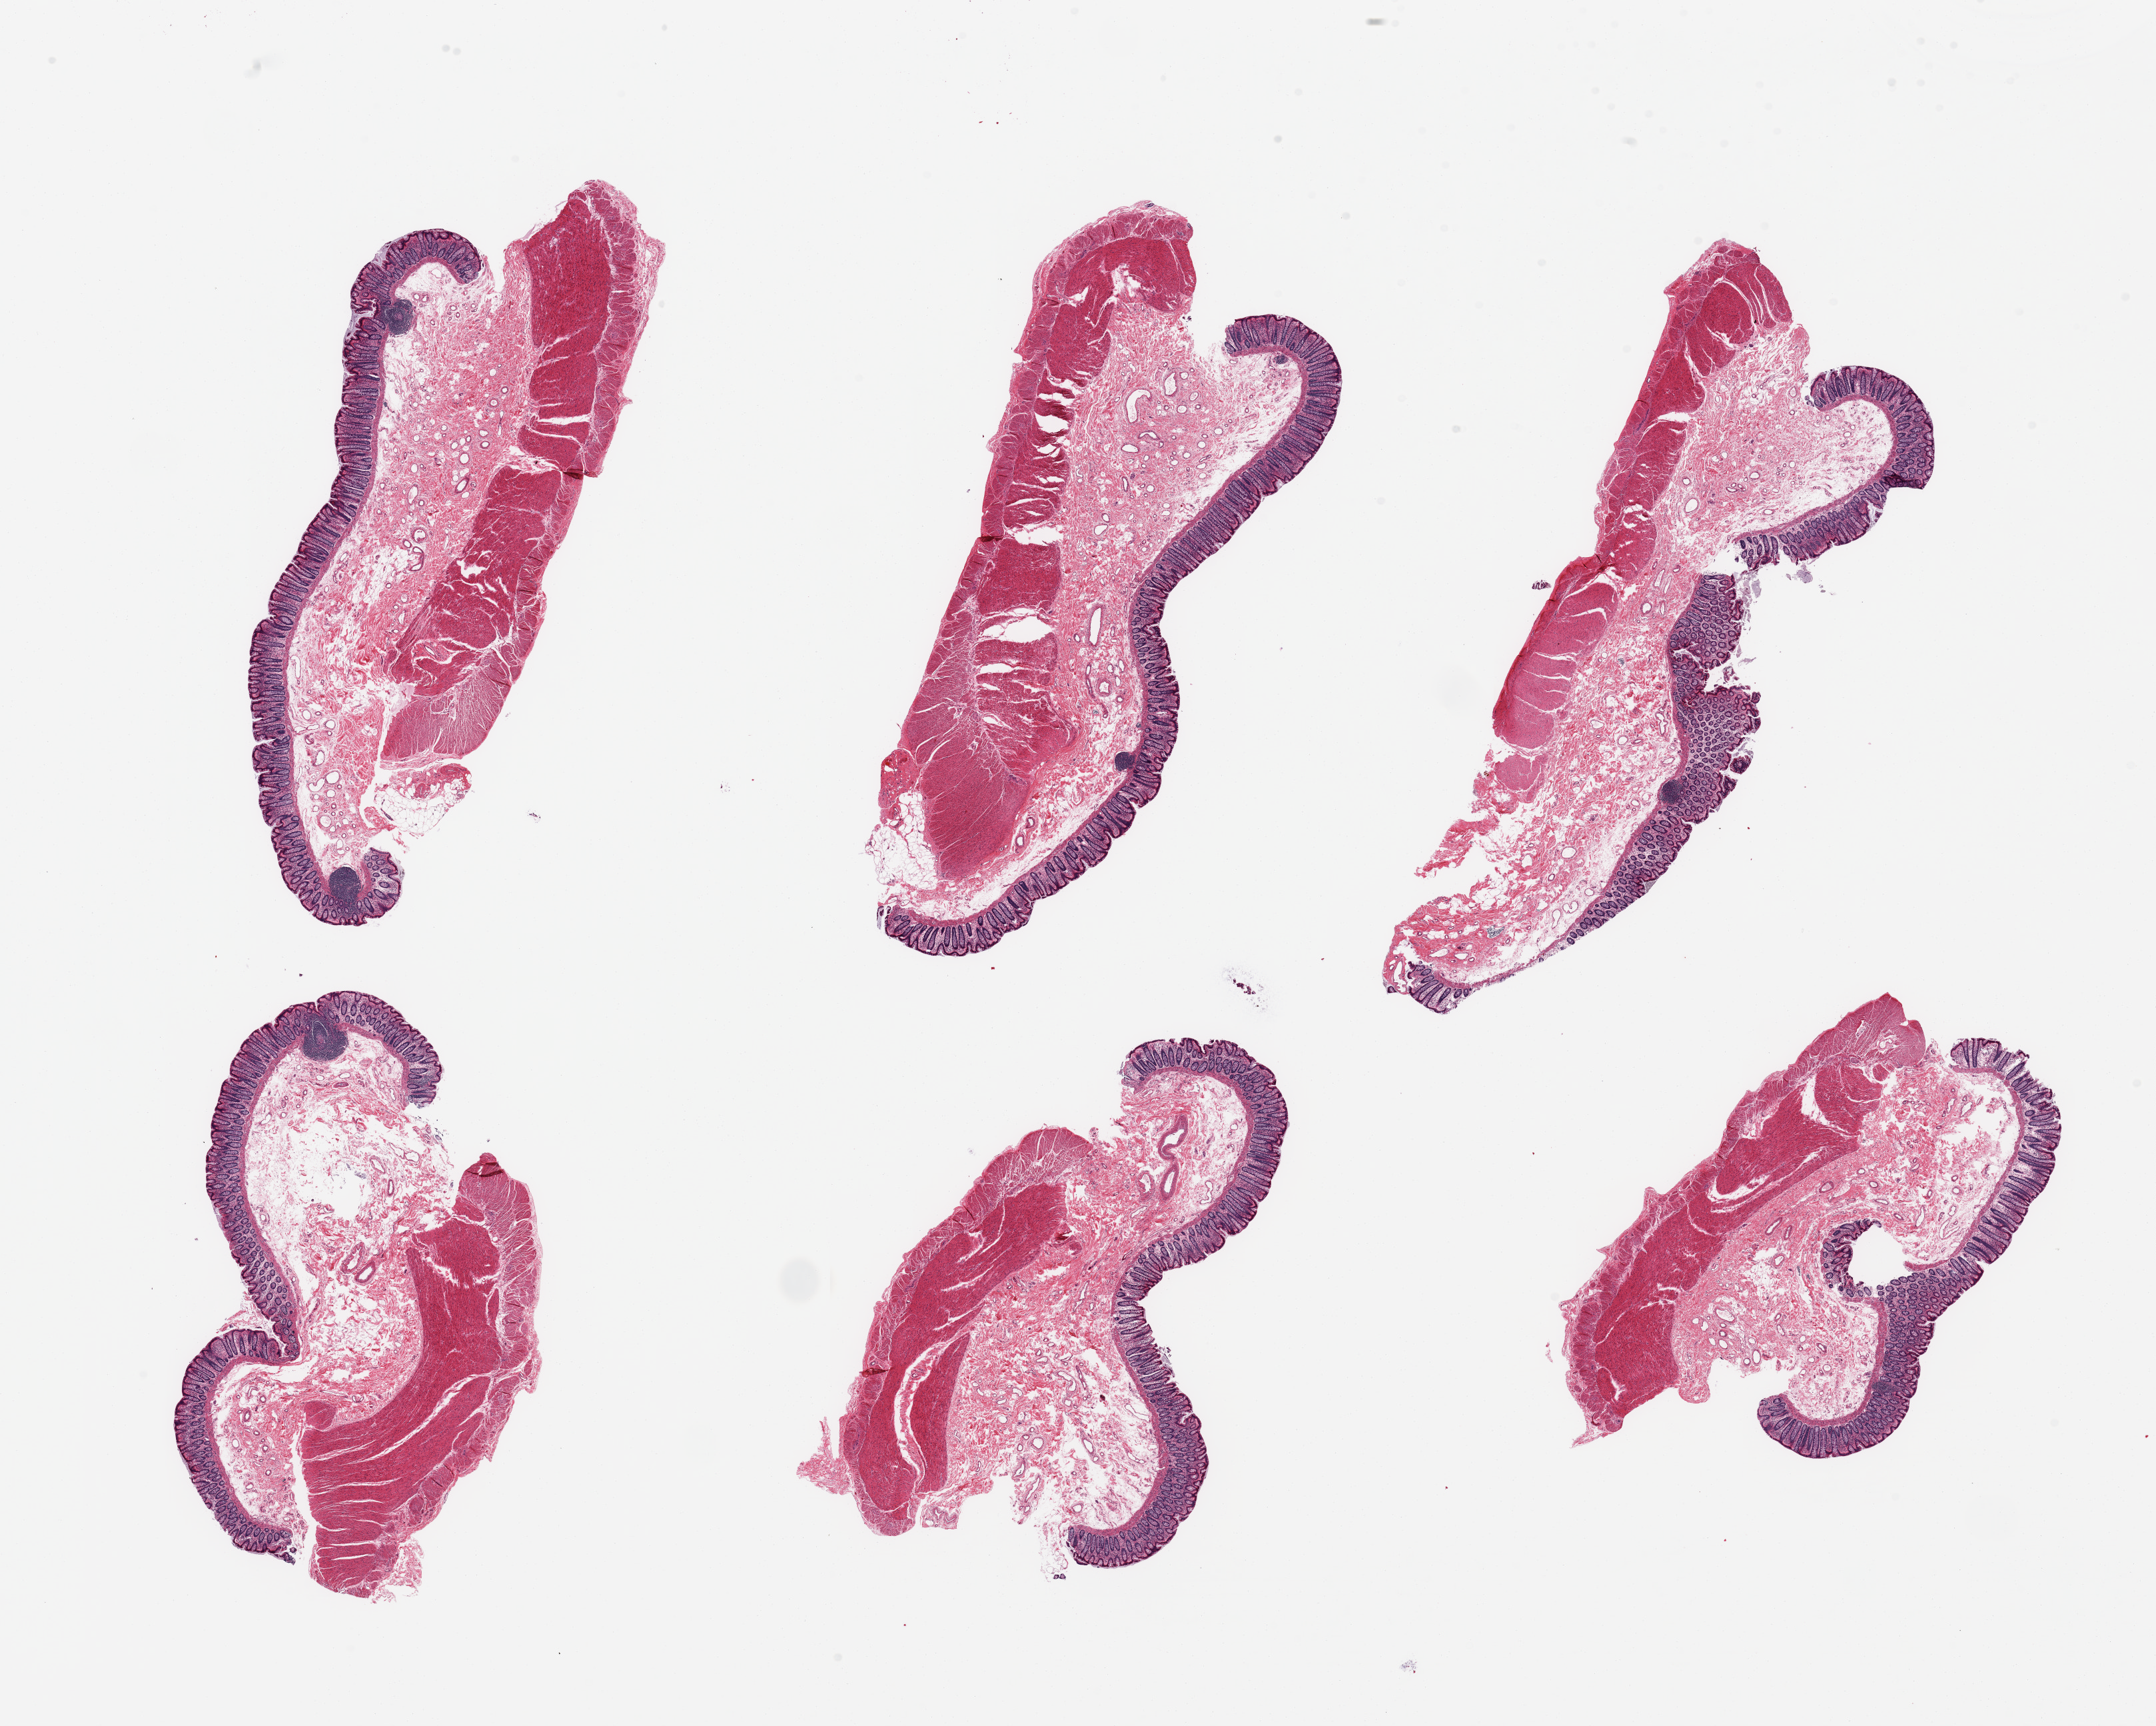
Digitized hematoxylin and eosin (H&E)-stained section, low-resolution overview of the scanned area, about 25.6 x 20.5 mm (slide scanned at 20x), PAXgene-fixed paraffin-embedded (PFPE) section, section of transverse colon (target tissue), donor tissue sample.
Review note (as recorded): 6 pieces; well preserved mucosa; thick submucosa up to 1.6 mm.